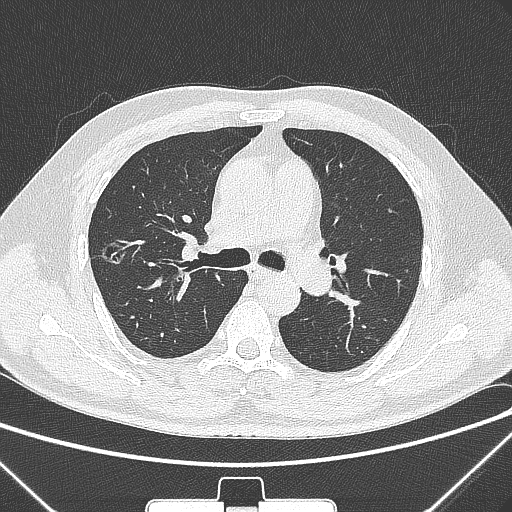
Chest CT, one axial slice. Slice 195 of 320 in the series (ordered by position). 120 kVp. Lung window (W 1500 / L -600 HU). 1 mm slice thickness. 512 × 512 image matrix, field of view 350 × 350 mm. Male patient, age 58 years. From the clinical record (not read from this slice): clinical TNM (as recorded): T1c N0 M0; histopathological grade: G2.
Outlined on this slice (bounding box drawn by a radiologist):
- lung tumour (recorded histology: adenocarcinoma): bounding box [x1, y1, x2, y2] px = [94, 230, 132, 275]